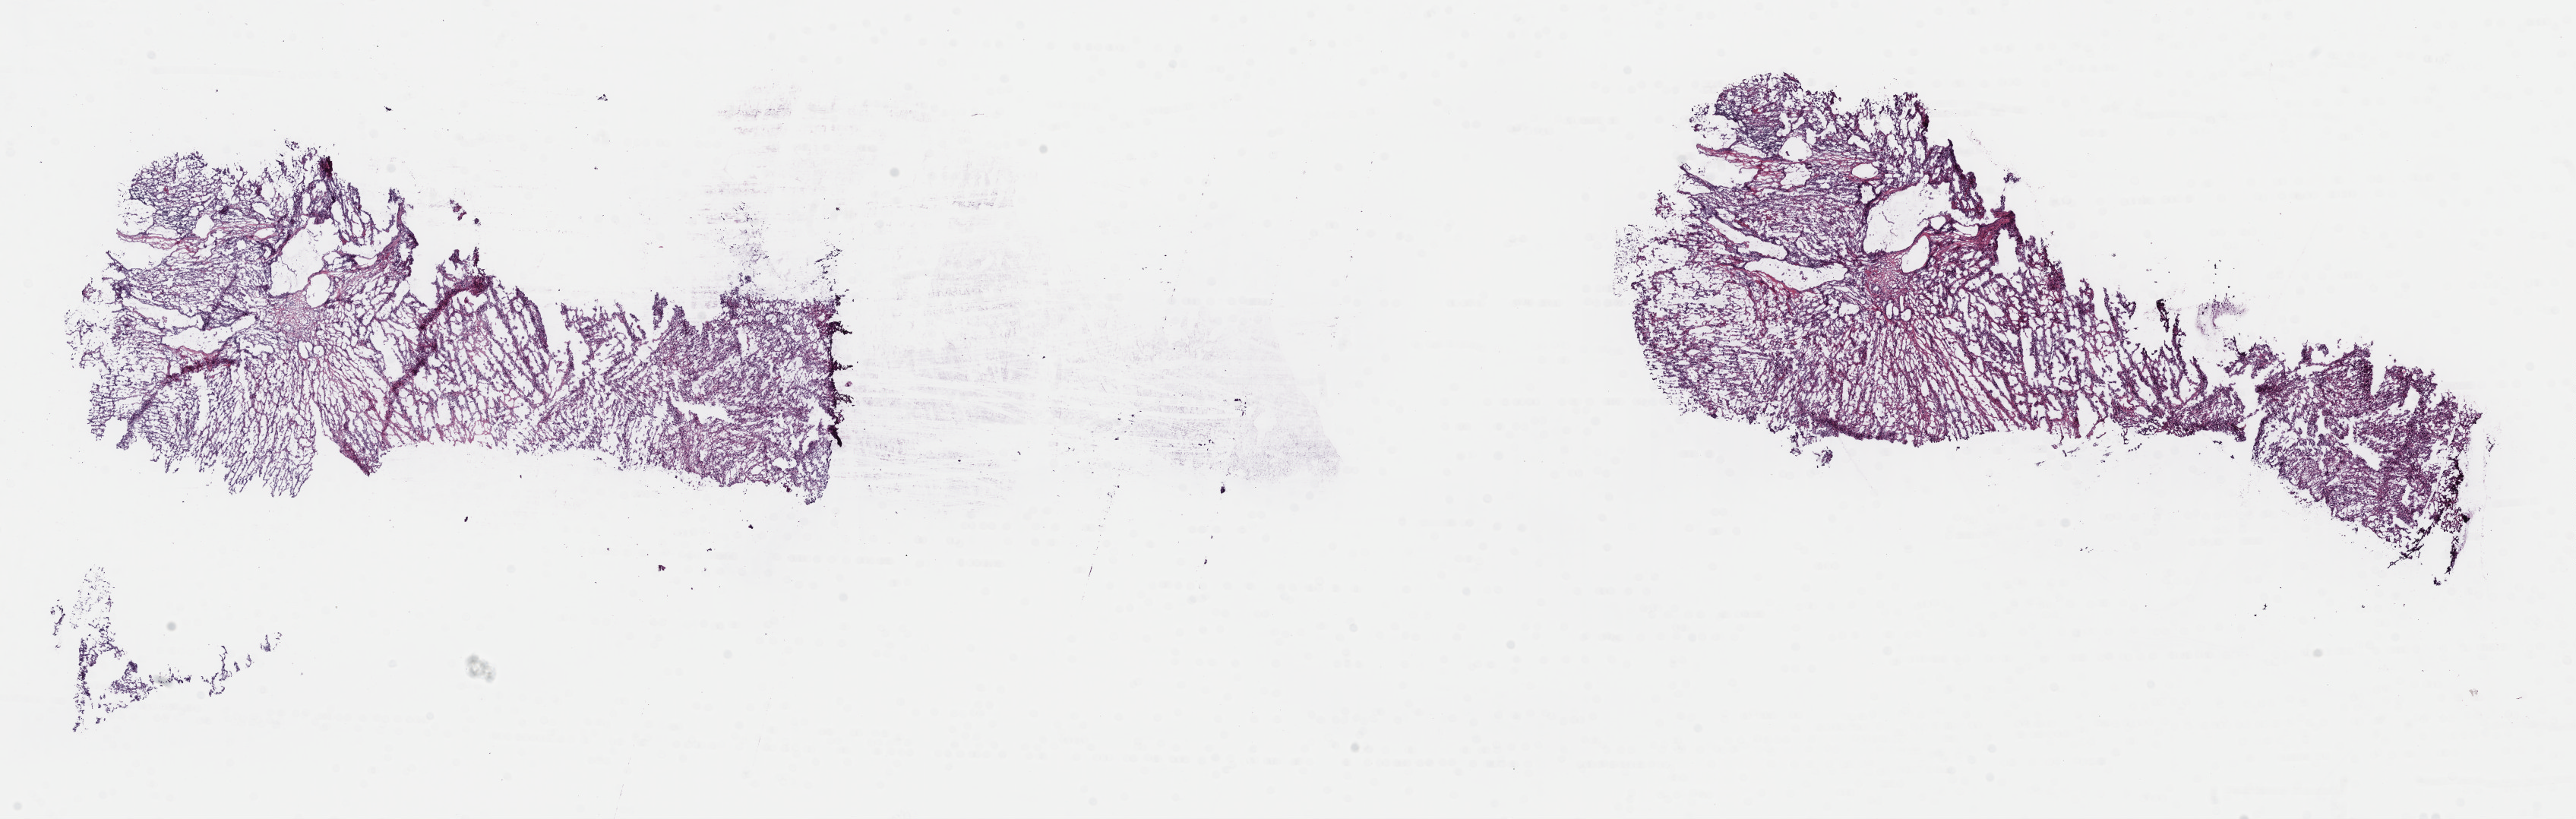
Digitized Hematoxylin and eosin (H&E) stained tissue section (whole slide) — whole scanned area (about 26.8 x 8.5 mm, slide scanned at 40x) shown as a low-resolution overview; frozen section from the top of the tissue portion; primary tumour sample from the adrenal cortex. Female patient; age at initial diagnosis 83 years. Composition of this section per pathologist review: tumour cells 80%, tumour nuclei 90%, normal cells 0%, stromal cells 20%, necrosis 0%. Infiltration values recorded for this section: lymphocyte infiltration 0%, monocyte infiltration 0%, neutrophil infiltration 0%.
* diagnosis: Adrenal cortical carcinoma (cortex of adrenal gland)